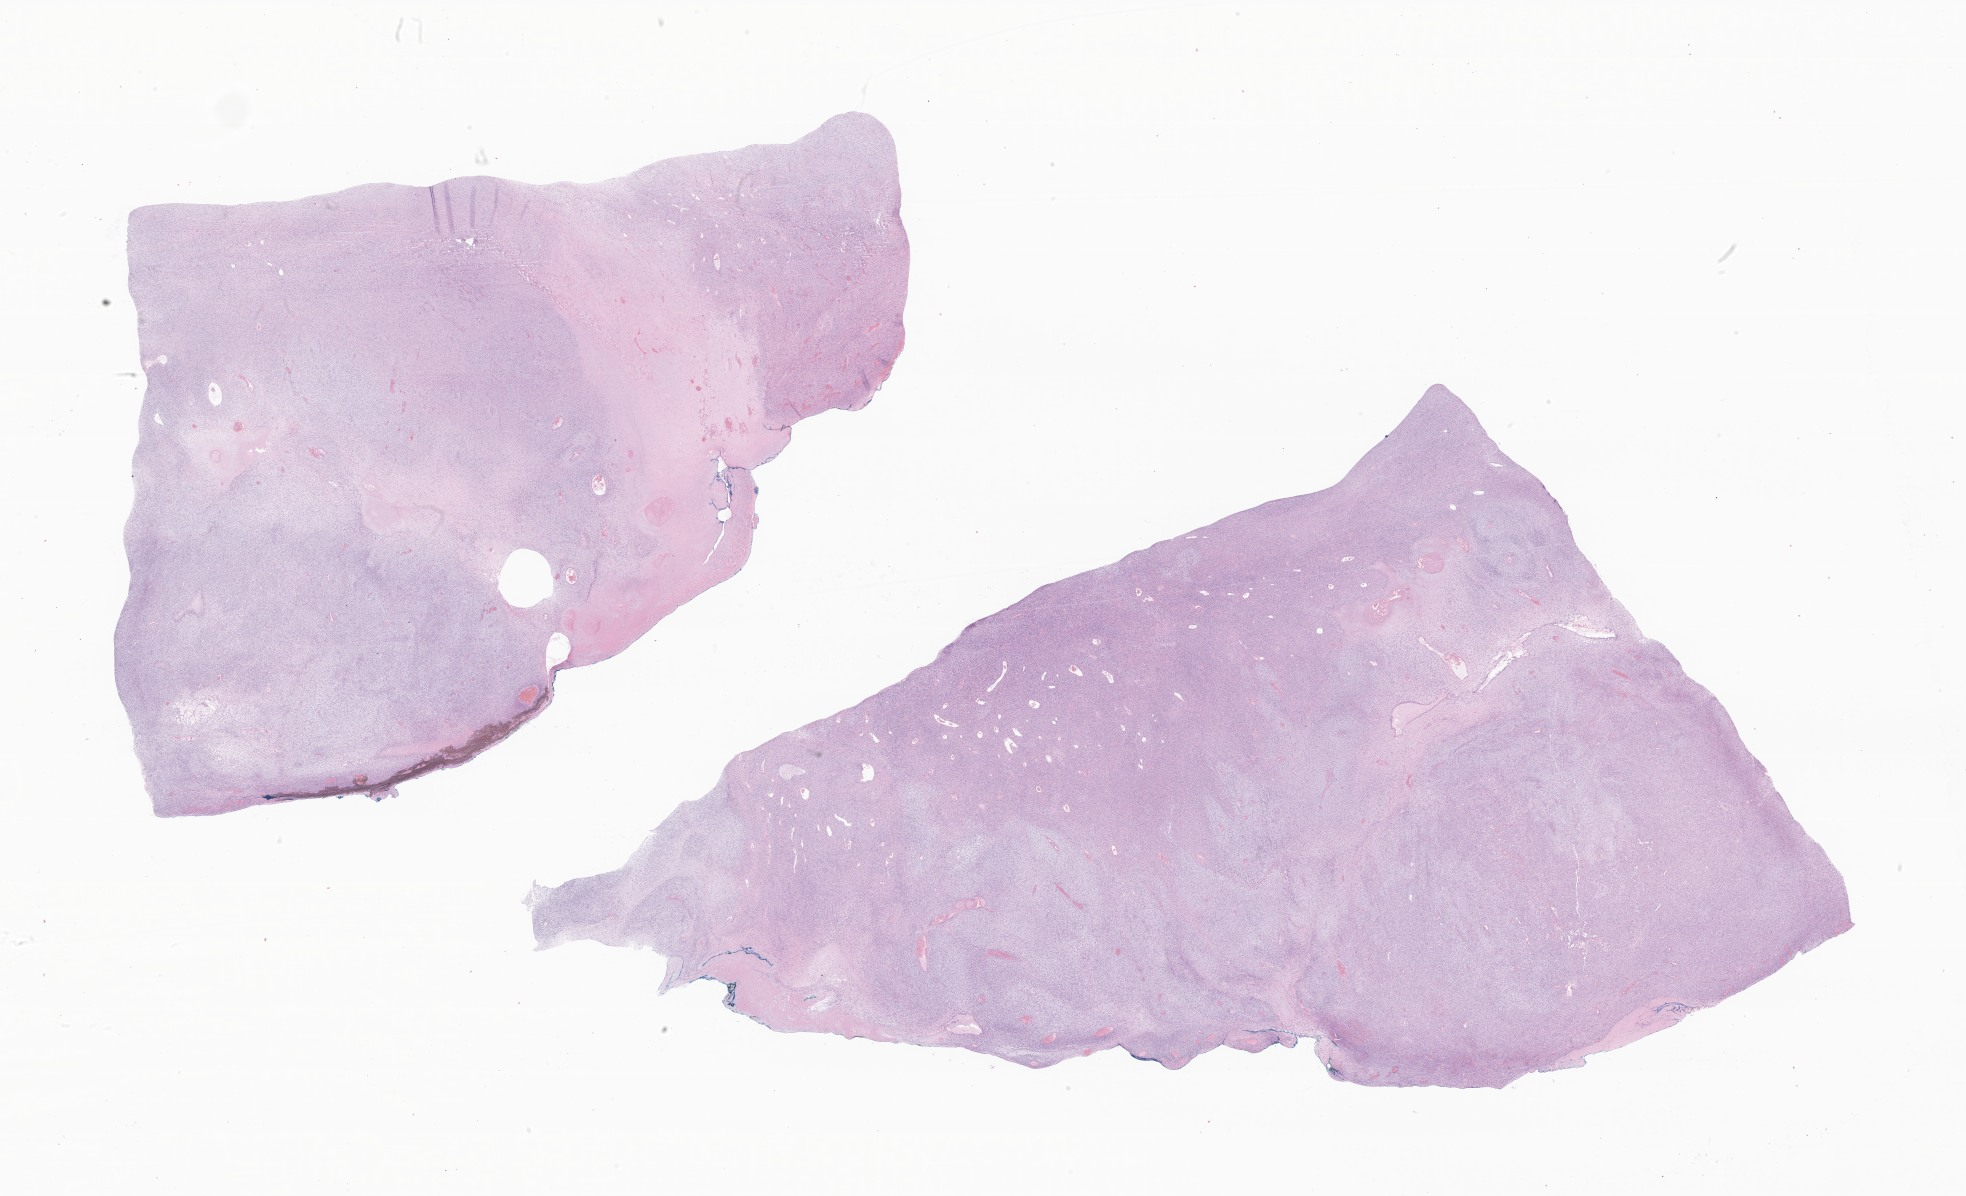
Whole-slide image, haematoxylin and eosin stain of tumor tissue from the mediastinum, a low-resolution overview of the entire scanned area, about 33.2 x 20.2 mm; FFPE section. Female patient, age 265 months (22 years 1 month).
Recorded diagnosis: Malignant peripheral nerve sheath tumor w. rhabdomyoblastic diff.